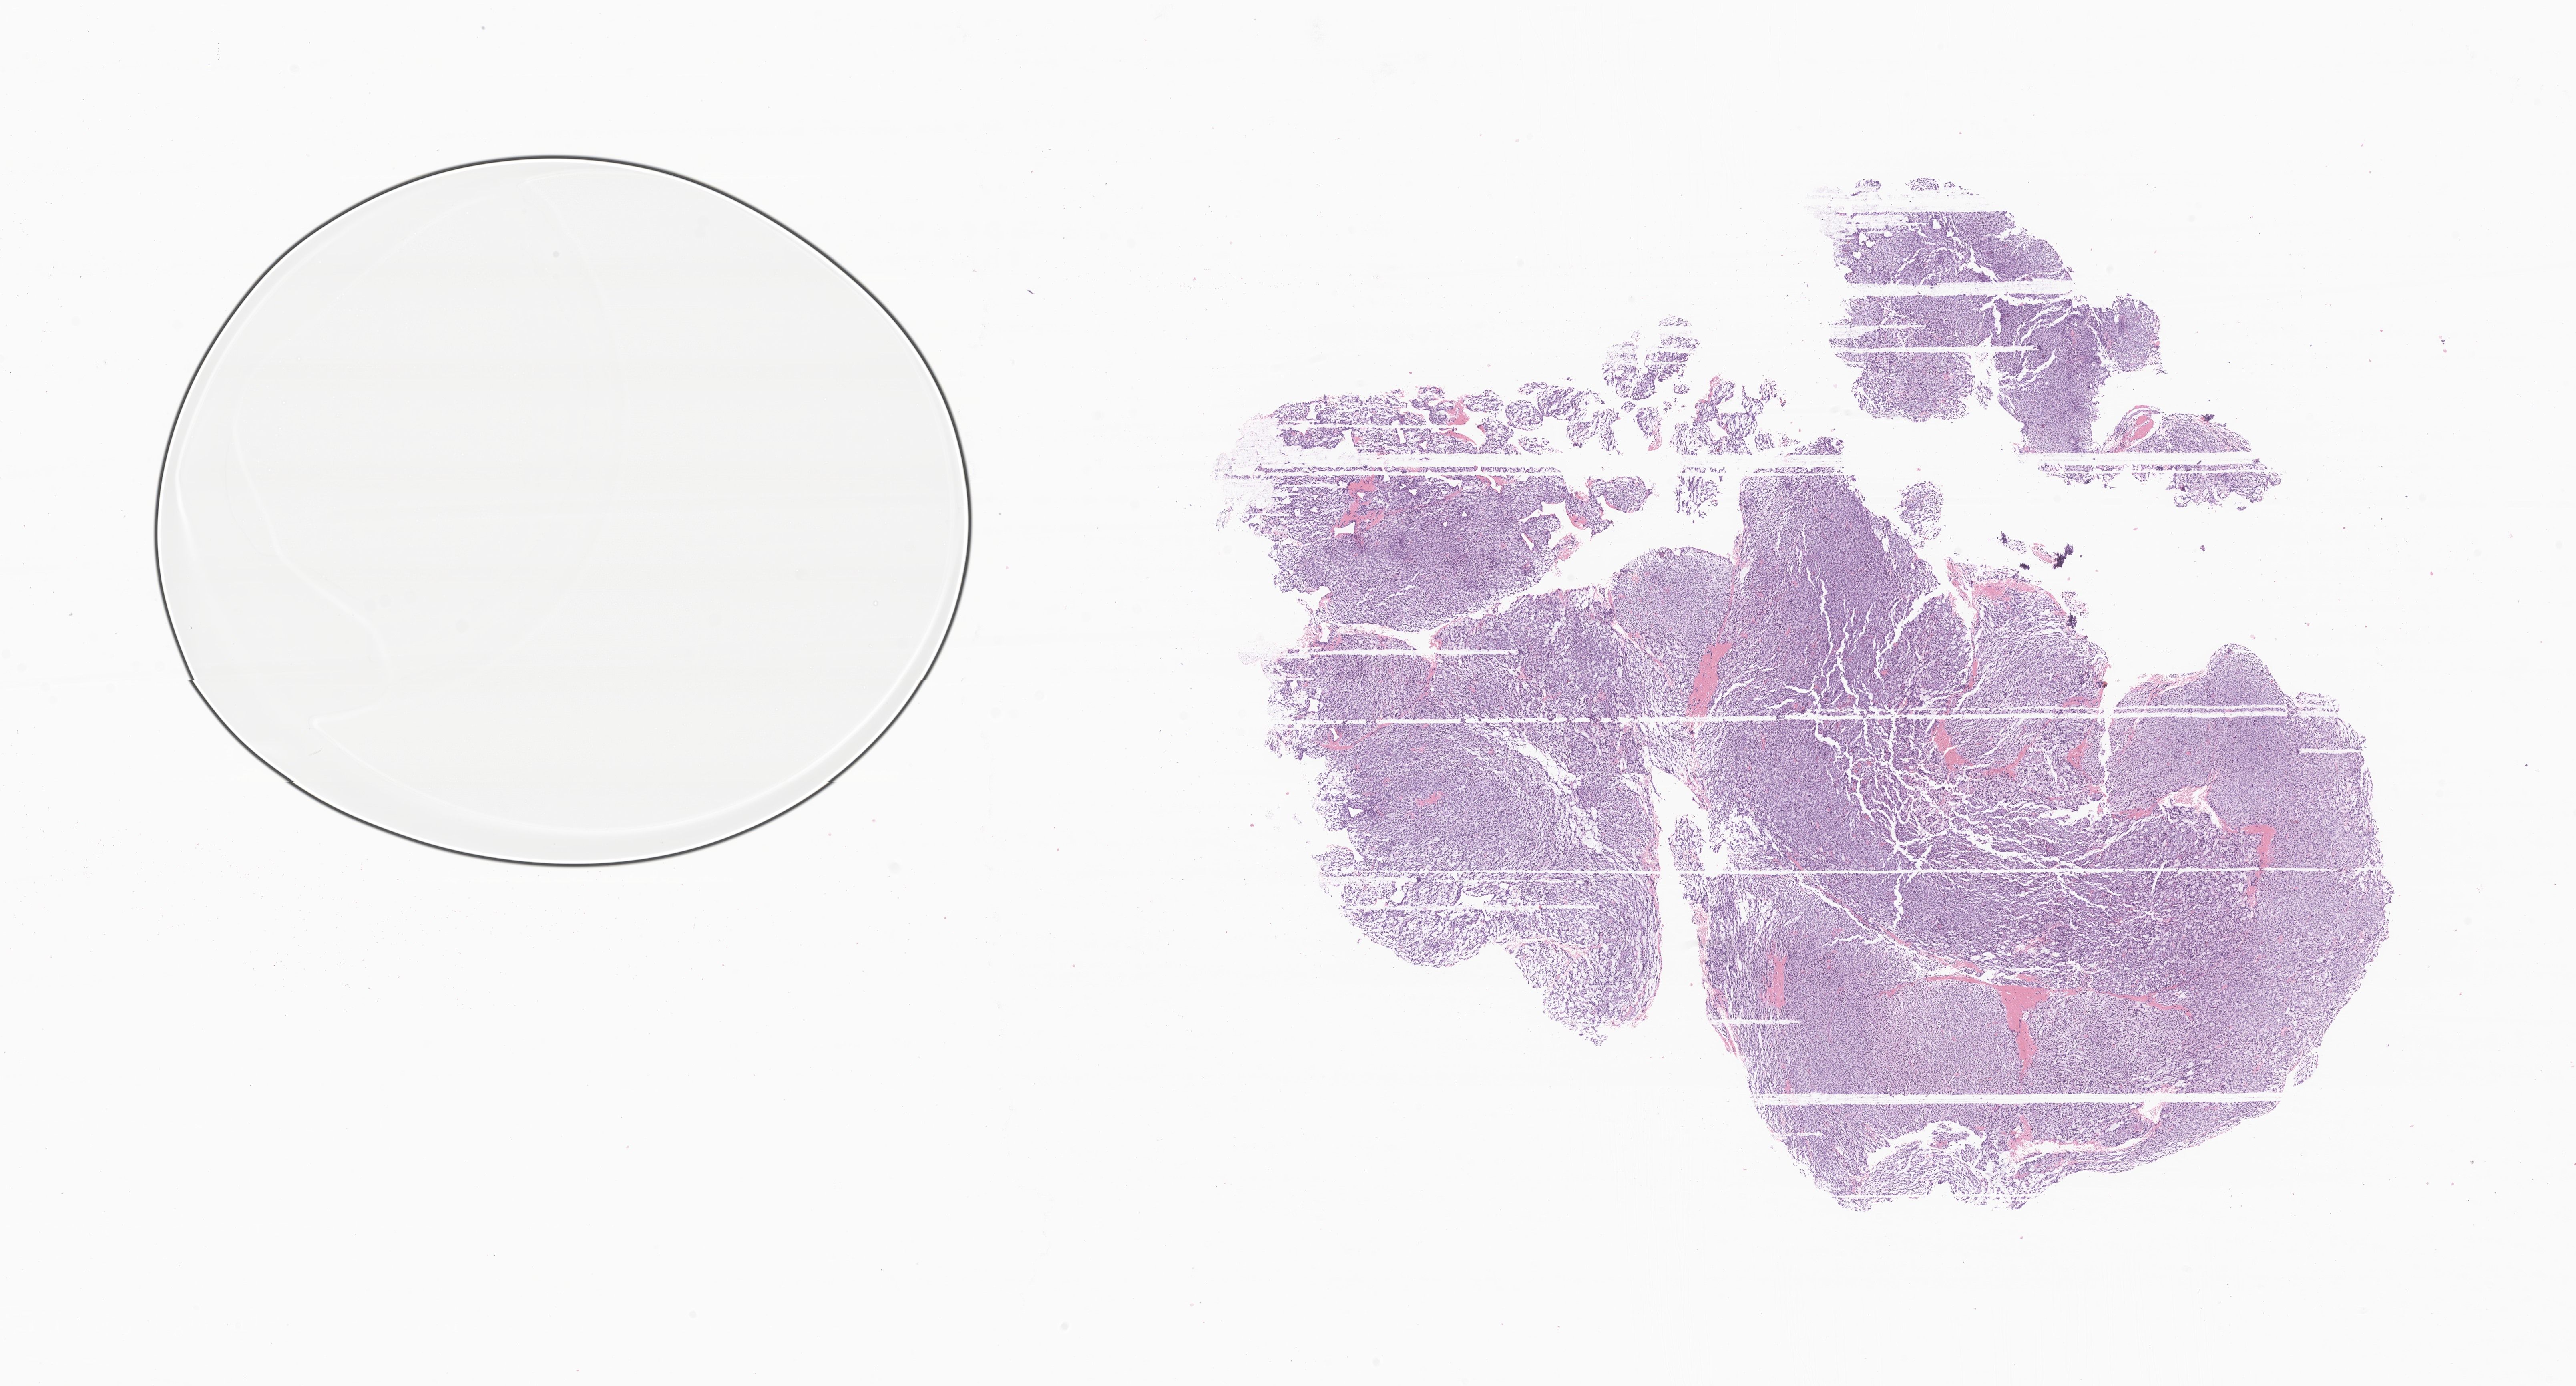
Whole-slide image, hematoxylin and eosin (H&E) stain of tumor tissue from the cerebrum — low-resolution overview of the scanned area, about 27.1 x 14.6 mm; formalin-fixed paraffin-embedded section. Patient female; age 158 months (13 years 2 months).
Recorded diagnosis: Glioma, malignant.